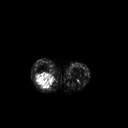
FDG PET of an extremity soft-tissue mass (from a PET/CT study), one axial slice. Slice 178 of 267 in the series (ordered by position). 3.27 mm slice thickness. 128 × 128 image matrix, field of view 500 × 500 mm. Female patient, age 62 years. Case-level facts recorded for this patient, not image findings: histological type: liposarcoma; site of the primary tumour: right thigh.
Annotated regions visible in this slice (expert contour drawn on MRI and transferred to this co-registered scan by the dataset authors):
- gross tumour volume (mass): box from (x=35, y=72) to (x=56, y=90) px